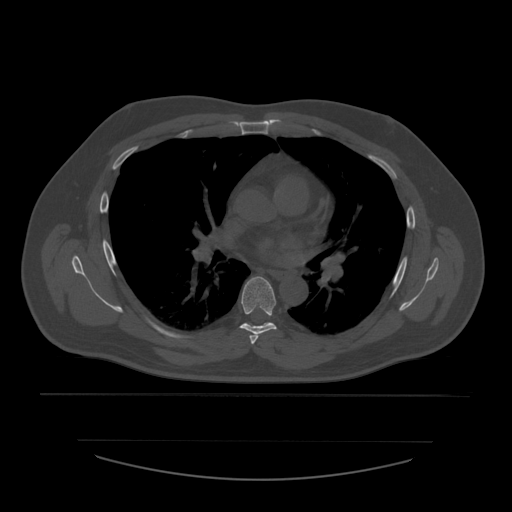
CT including the spine, one axial slice. Slice 379 of 532 in the series (ordered by position). 120 kVp. Bone window (W 1800 / L 400 HU). 512 × 512 image matrix, field of view 441 × 441 mm. Patient age 44 years. Case-level facts recorded for this patient, not image findings: primary cancer: soft tissue sarcoma.
Annotated regions visible in this slice (semi-automatic segmentation, software-assisted and operator-edited):
- T5 vertebra: bounding box [x1, y1, x2, y2] px = [250, 334, 259, 345]
- T6 vertebra: [240, 277, 277, 335]